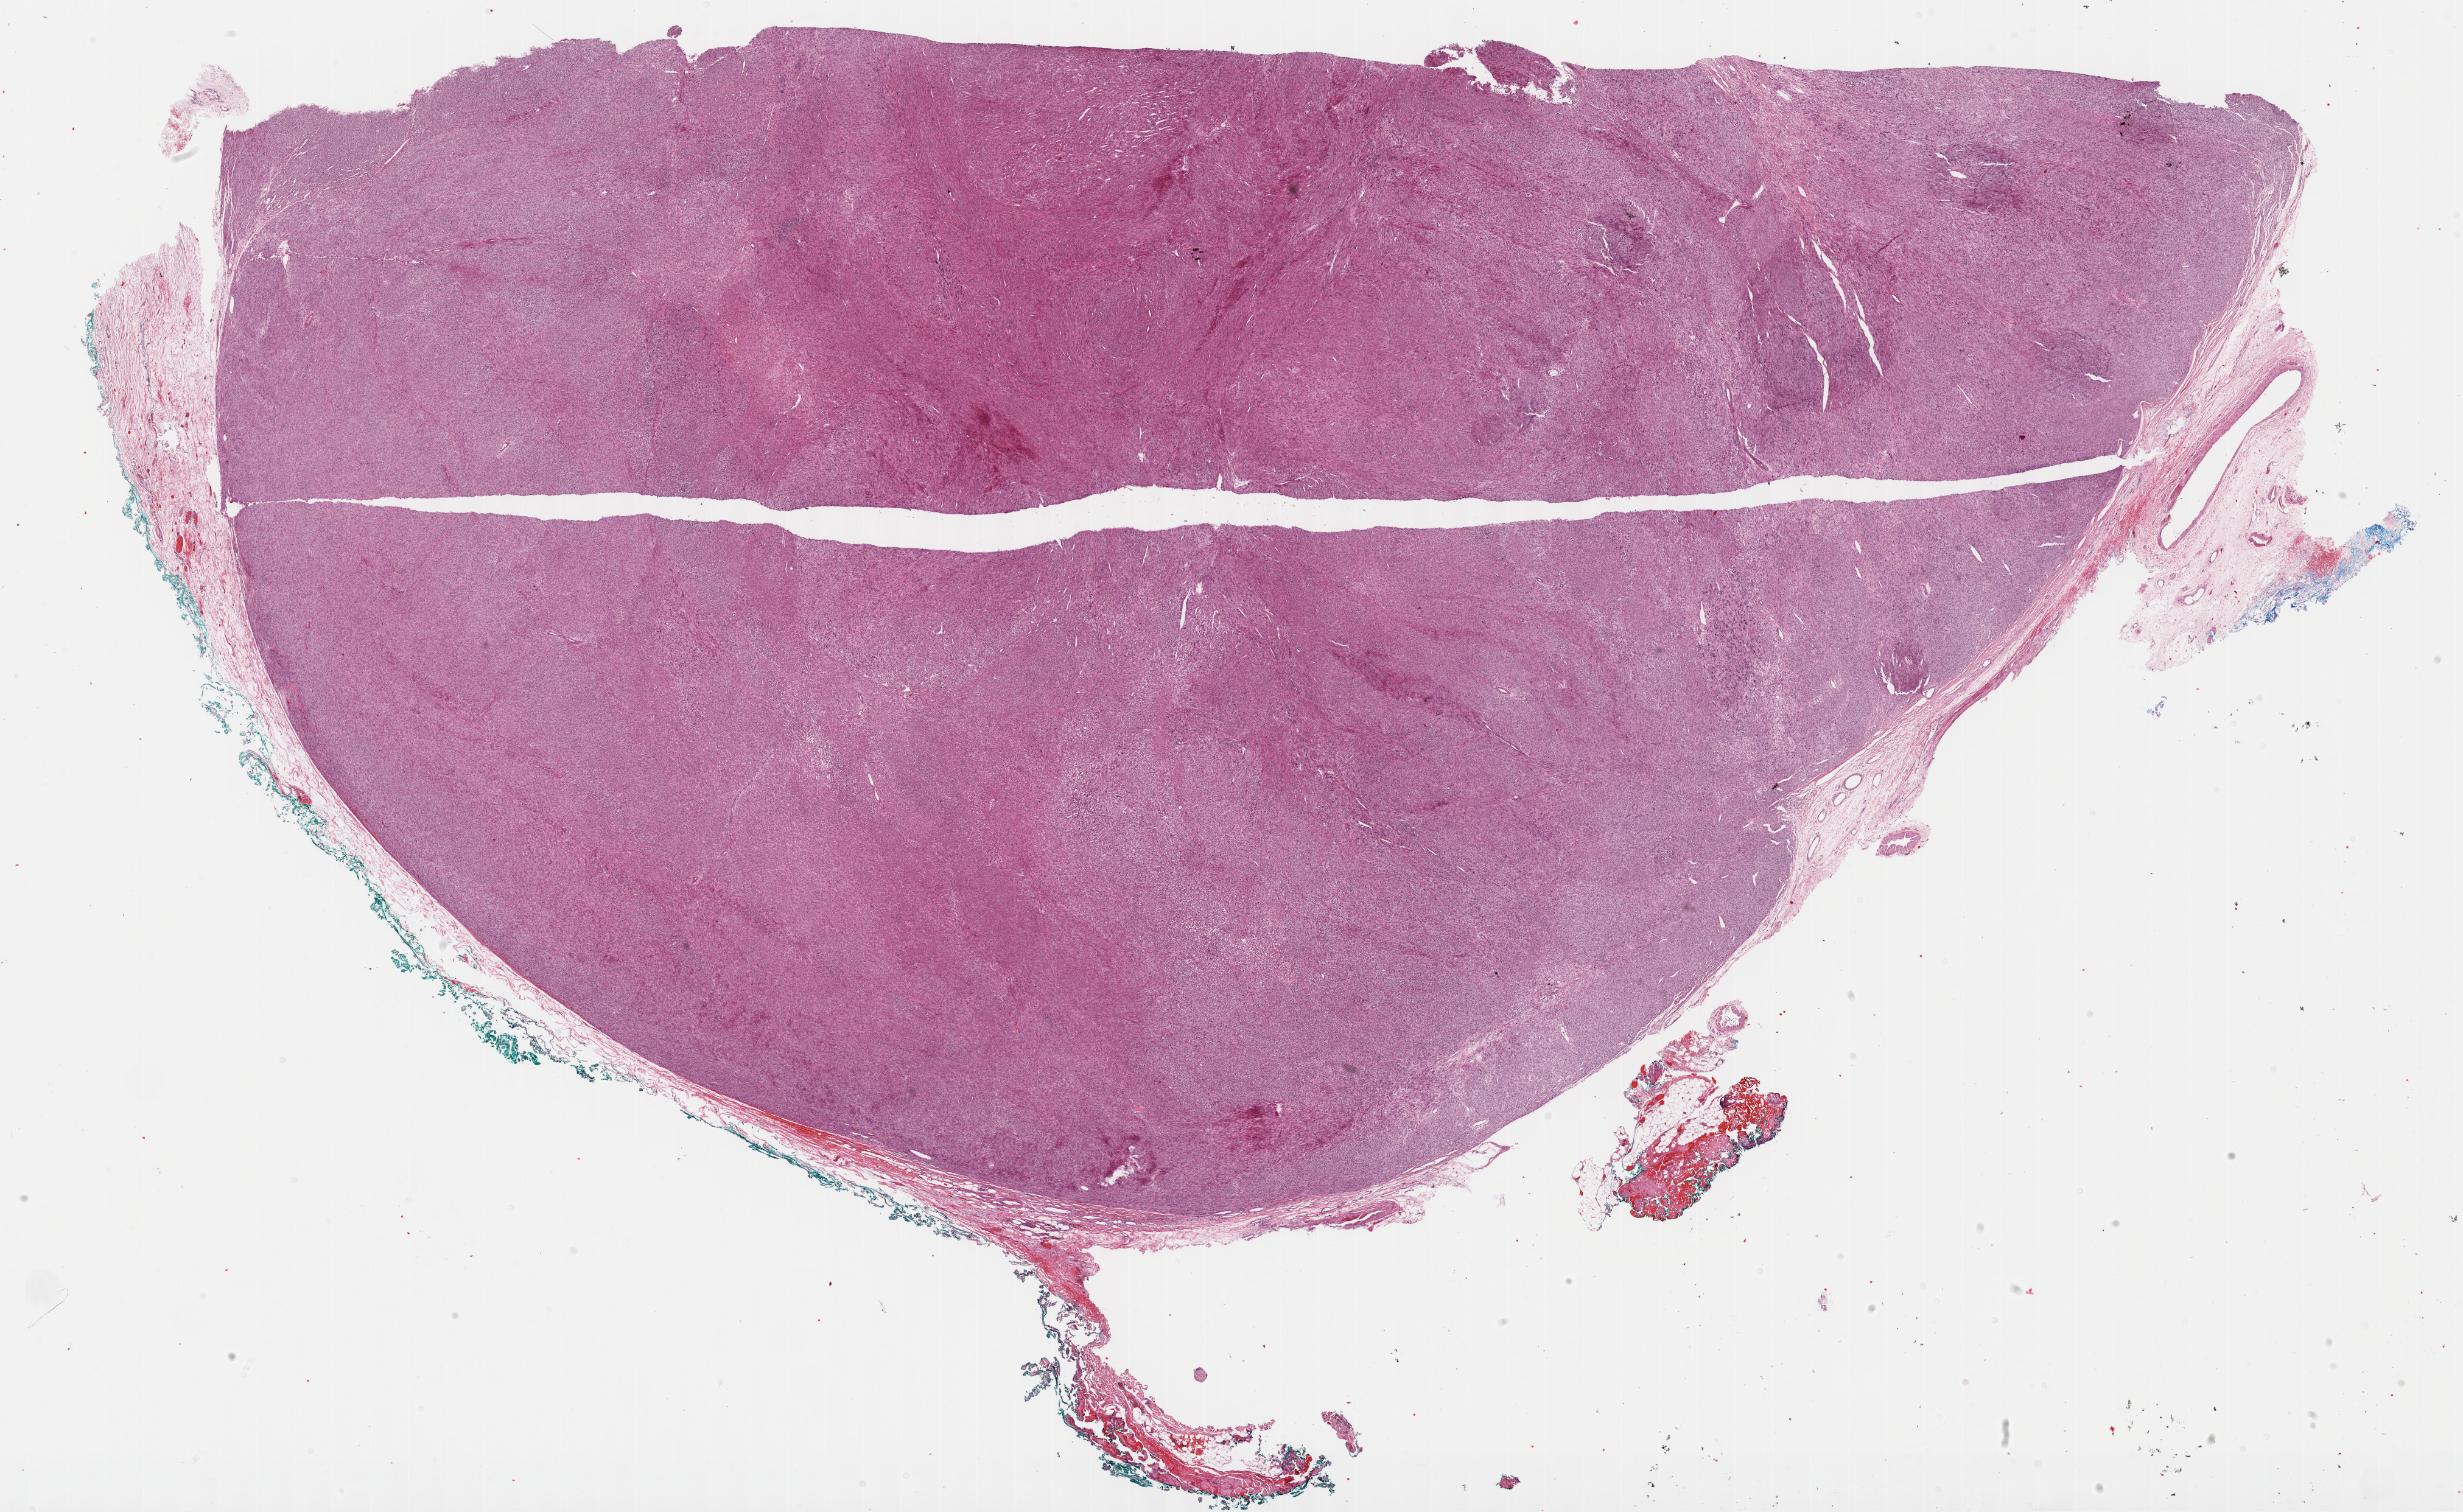
H&E-stained whole-slide image, shown as a low-resolution overview of the whole scanned area (about 32.7 x 20.1 mm). Formalin-fixed paraffin-embedded (FFPE) diagnostic section. Retroperitoneum and peritoneum, primary tumour sample. Female patient; age at initial diagnosis 37 years.
Histologic diagnosis: Leiomyosarcoma, NOS (retroperitoneum).